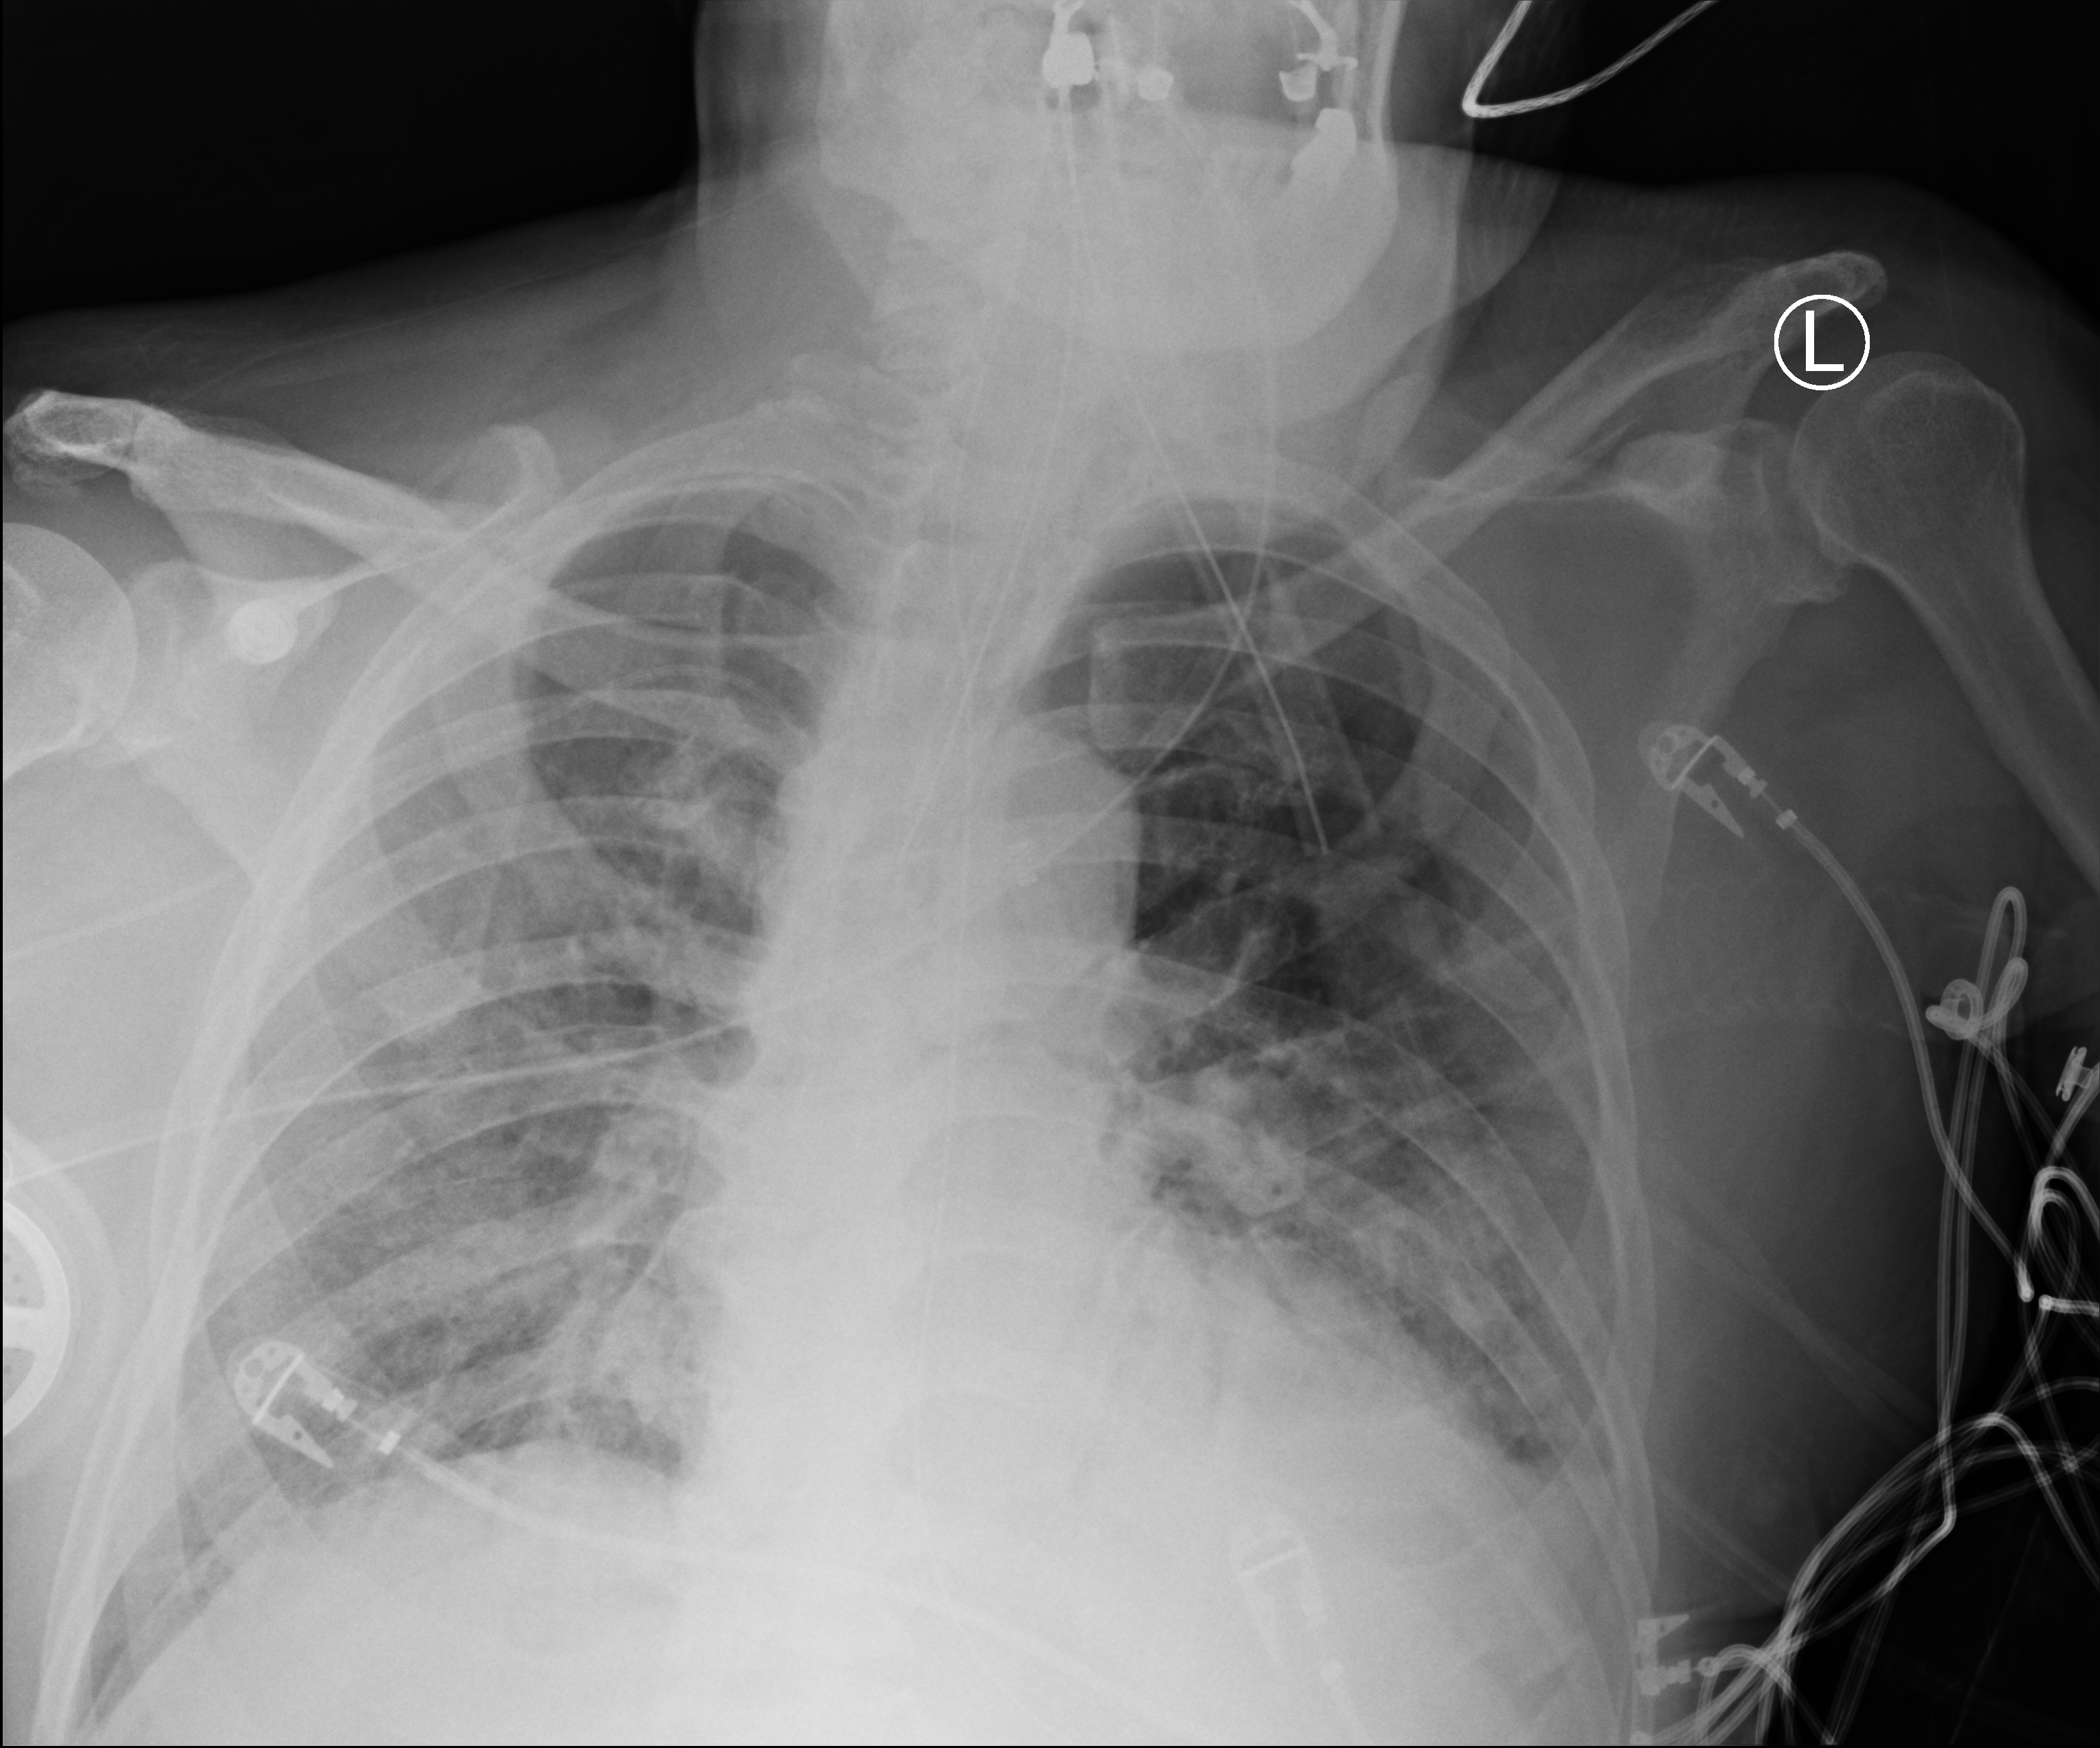
Portable chest radiograph. Male patient hospitalised with COVID-19, age 75–90 years.
Hospital-stay facts (about this admission, not read from this image; timing relative to this image not recorded):
- mechanically ventilated during this hospital stay: yes
- length of hospital stay: 33 days